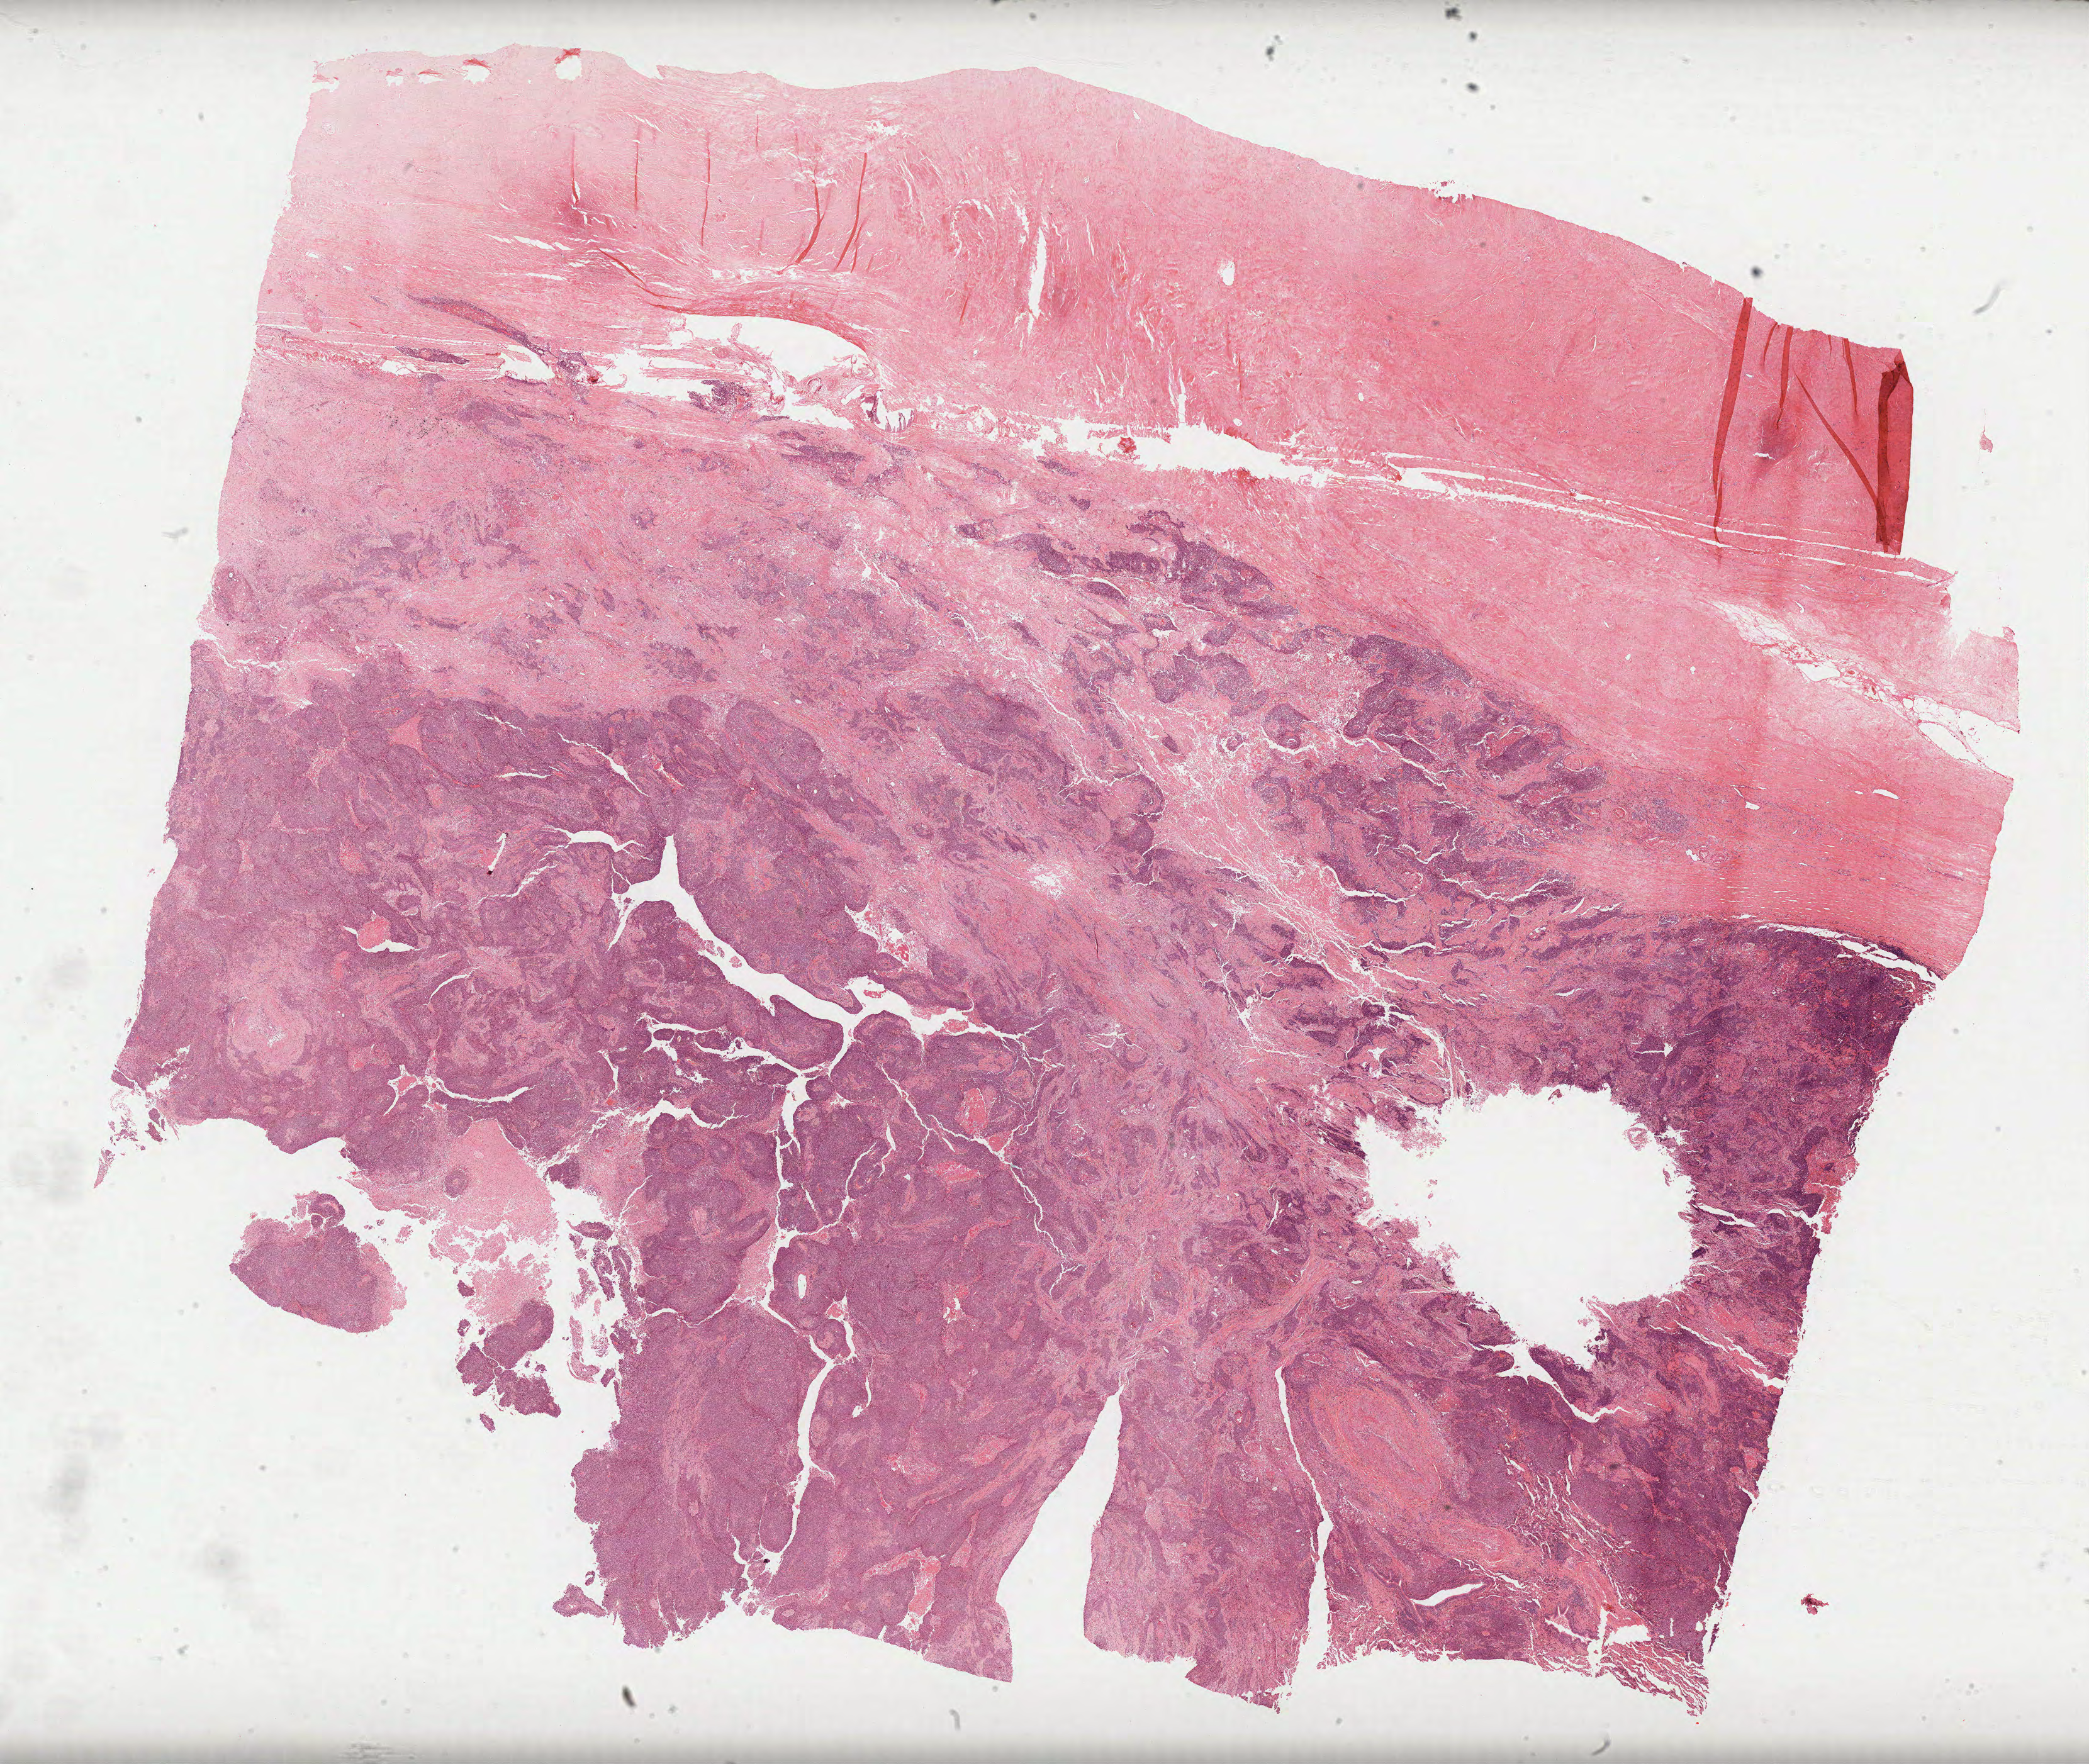
Digitized H&E-stained tissue section (whole slide), low-resolution overview of the scanned area, about 26.8 x 22.6 mm (acquisition: 40x scan), formalin-fixed paraffin-embedded (FFPE) diagnostic section, lung, primary tumour sample. Patient: male, age at initial diagnosis 81 years.
- TNM: T3 N0 M0
- diagnosis: Squamous cell carcinoma, NOS (lower lobe, lung)
- AJCC pathologic stage: IIB